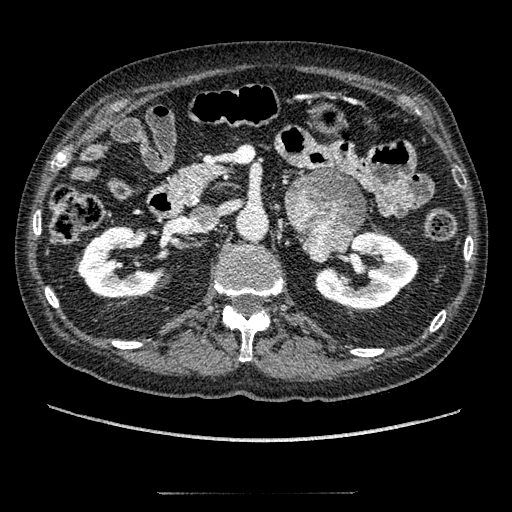
Contrast-enhanced abdominal CT, one axial slice. Position 102 of 274 along the scan axis. Reconstruction kernel STANDARD. 120 kVp. Intravenous contrast given. Soft-tissue window (W 400 / L 40 HU). 1.25 mm slice thickness. 512 × 512 image matrix. Male patient, age 69 years. Case-level facts recorded for this patient, not image findings: diagnosis: adrenocortical carcinoma; tumour side: left adrenal; tumour size at pathology: 6.1 cm; Ki-67 index: 10 %; stage (as recorded): 3.
Outlined on this slice (semi-automatically segmented with operator editing):
- mass: box from (x=286, y=171) to (x=362, y=261) px